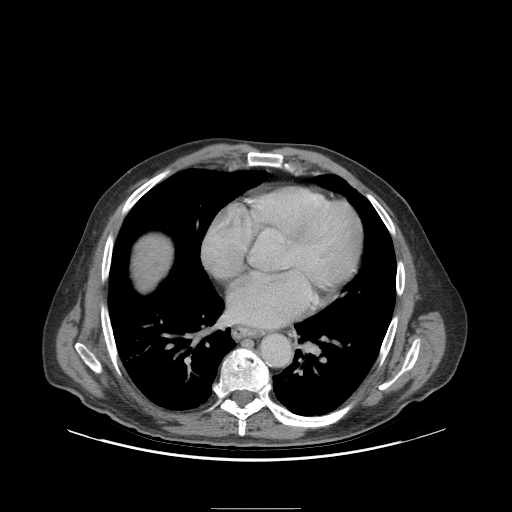
Contrast-enhanced abdominal CT (liver protocol), one axial slice; position 100 of 105 along the scan axis; reconstruction kernel STANDARD; soft-tissue window (W 400 / L 40 HU); 2.5 mm slice thickness; 512 × 512 image matrix. From the clinical record (not read from this slice): diagnosis: hepatocellular carcinoma (patient treated with transarterial chemoembolisation; whether this scan precedes or follows treatment is not stated here); TNM stage (as recorded): Stage-I; Child-Pugh class: A; tumour nodularity: uninodular.
Outlined on this slice (semi-automatically segmented with operator editing):
- liver parenchyma outside the tumour (the mass and vessels are separate outlines, so this box may not span the whole liver): bounding box (x1, y1, x2, y2) in pixels: (132, 236, 172, 290)